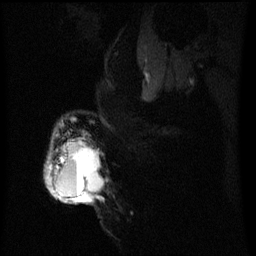
Breast MRI (dynamic contrast-enhanced), one sagittal slice; dynamic contrast-enhanced series, image 2 of 3 at this slice position (ordered by acquisition); 1.5 T; TE 4.2 ms, TR 8 ms; 2.2 mm slice thickness; 256 × 256 image matrix, field of view 200 × 200 mm. Patient: female, 50 years.
Outlined on this slice (semi-automatically segmented with operator editing):
- analysis volume of interest (the breast-tissue region the enhancement analysis was run in; not a lesion): box from (x=48, y=134) to (x=104, y=203) px
- tumour enhancement mask (voxels above the 70 % enhancement threshold inside the analysis volume of interest): (x=48, y=142)–(x=96, y=203)